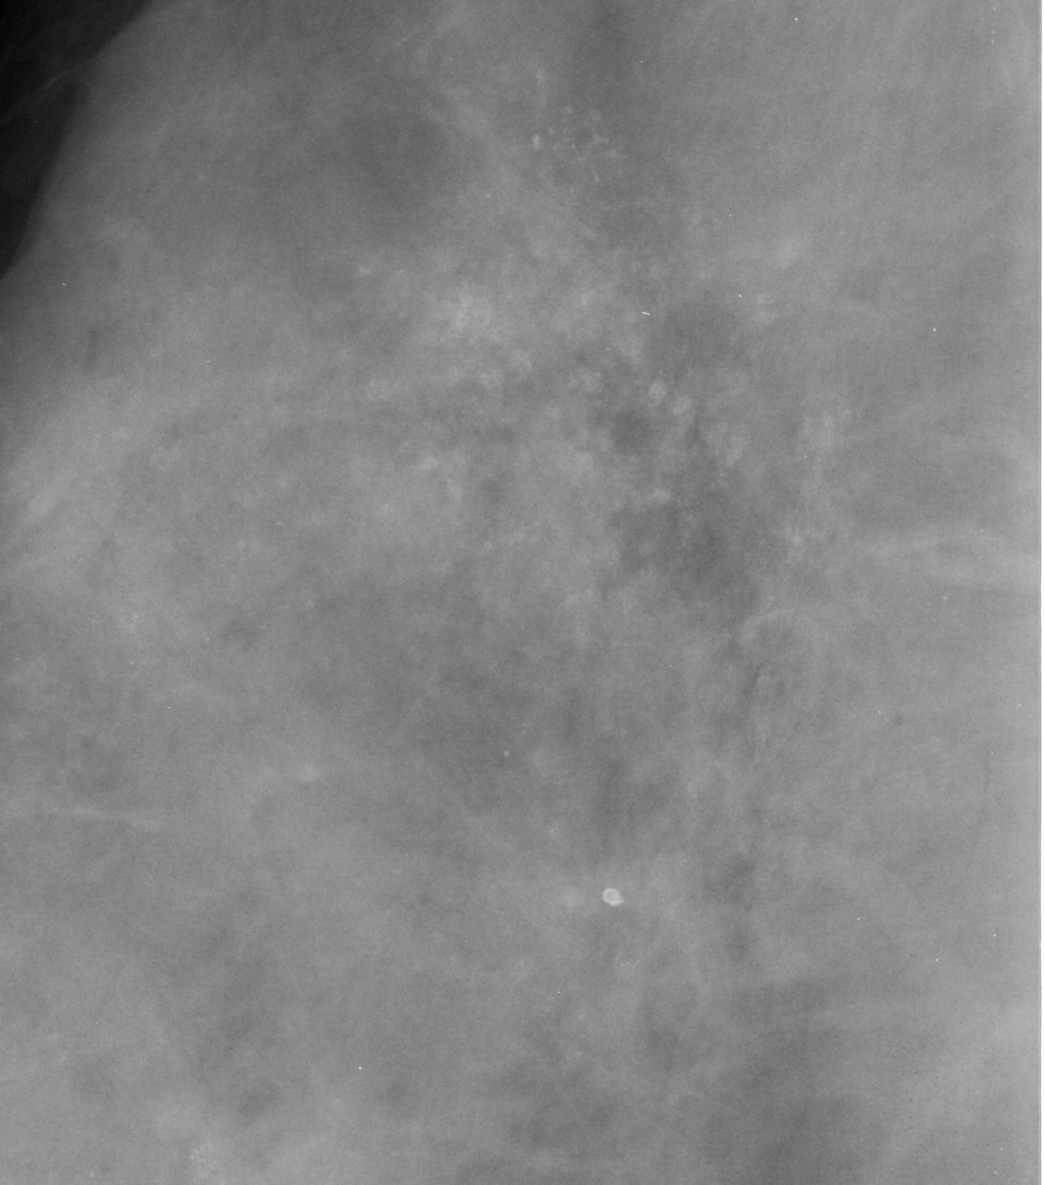
Crop from a digitized film mammogram around one marked abnormality; right breast; MLO view.
Calcifications, morphology punctate / amorphous, distribution regional; BI-RADS assessment category 4; pathology (as recorded): benign.